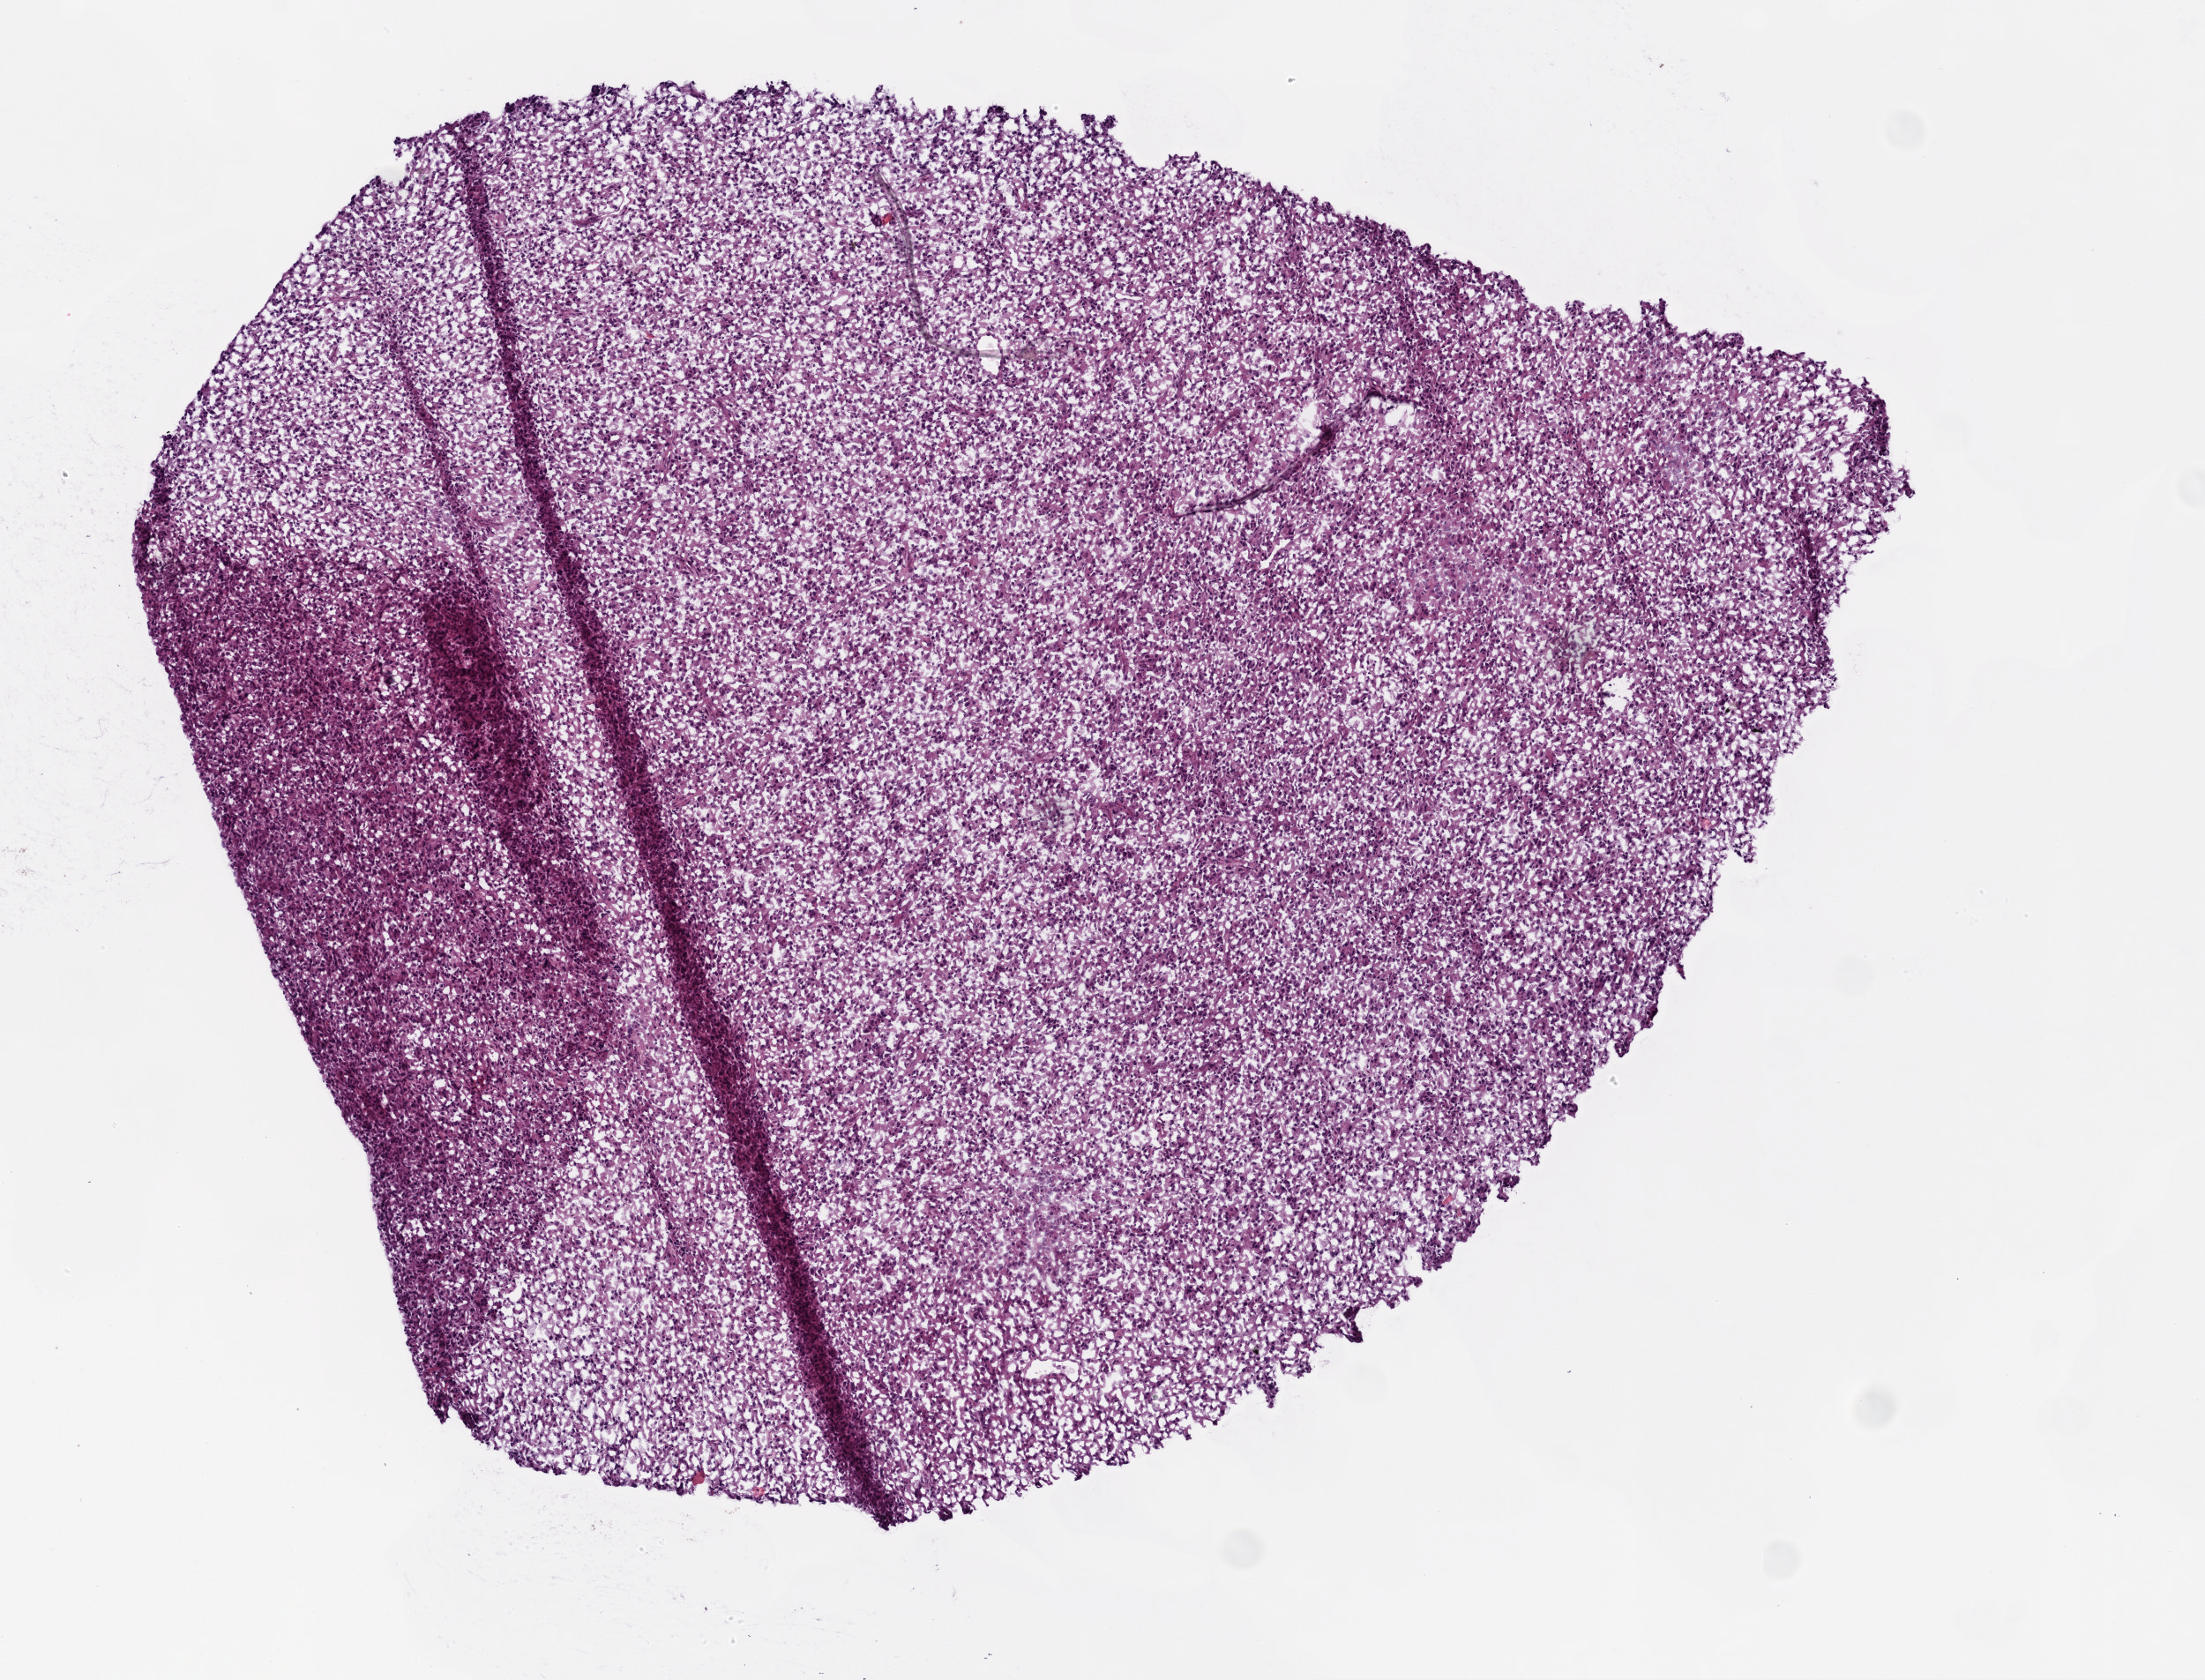
Digitized H&E tissue section (whole slide) — a low-resolution overview of the entire scanned area, about 5.0 x 3.8 mm (acquisition: 20x scan), frozen section from the top of the tissue portion, sample: primary tumour, brain. Male, age 73 years at initial diagnosis. Composition of this section per pathologist review: tumour cells 80%, tumour nuclei 90%, normal cells 10%, stromal cells 10%, necrosis 0%. Infiltration values recorded for this section: lymphocyte infiltration 100%.
• histologic diagnosis: Glioblastoma